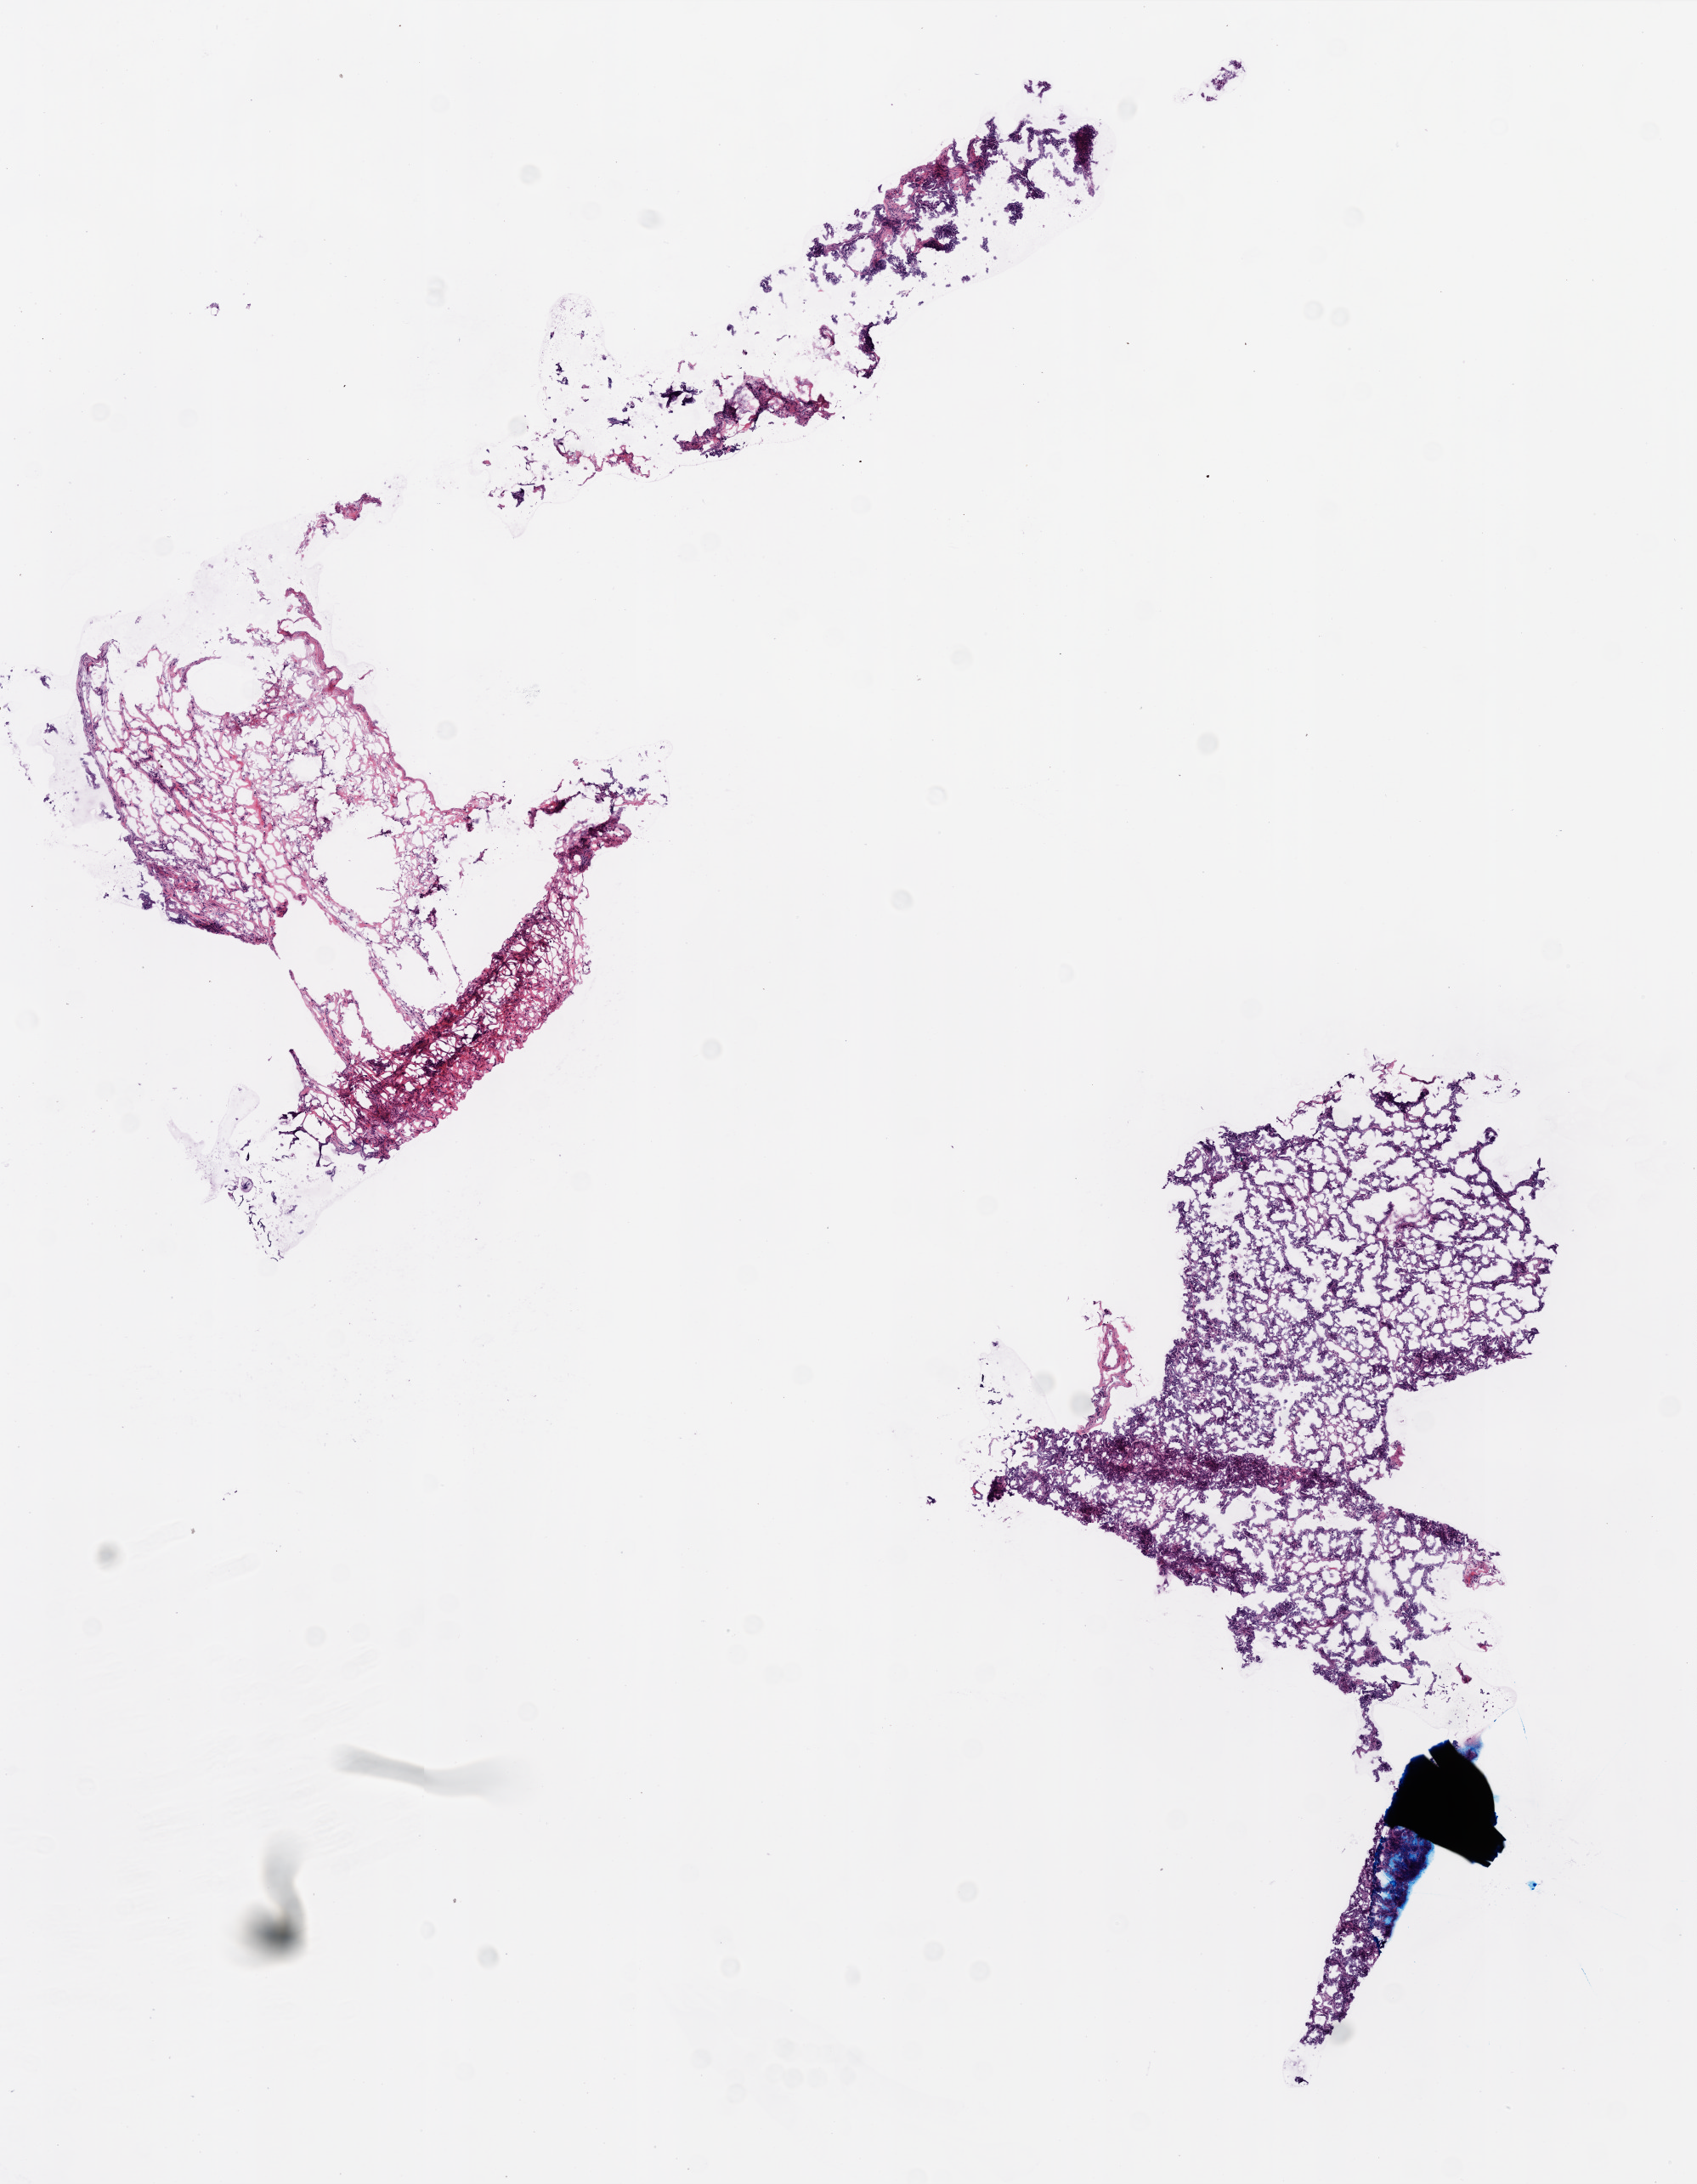
H&E-stained whole-slide image, a low-resolution overview of the entire scanned area, about 8.0 x 10.3 mm (from a 20x scan); frozen section from the top of the tissue portion; sample: primary tumour, ovary. Patient: female, age at initial diagnosis 53 years. Histologic grade: G3 (poorly differentiated). Slide review estimates, as recorded: tumour nuclei 90%, normal cells 0%, necrosis 1%.
Pathologic diagnosis: Serous cystadenocarcinoma, NOS. FIGO stage: IIIC.